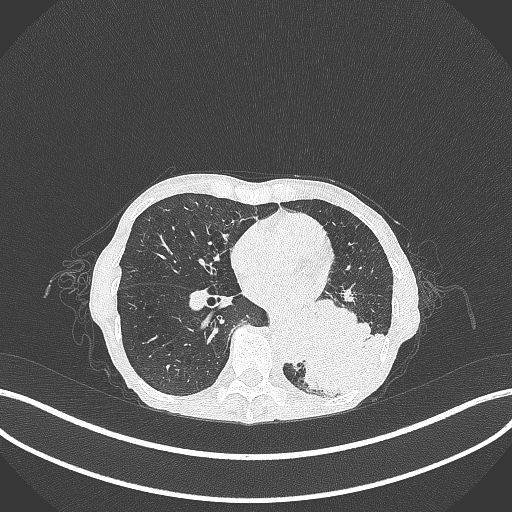
Chest CT, one axial slice; reconstruction kernel B70f; lung window (W 1500 / L -600 HU); 512 × 512 image matrix, field of view 400 × 400 mm. Female patient, age 70 years. From the clinical record (not read from this slice): clinical TNM (as recorded): T3 N0 M0; histopathological grade: G3.
Annotated regions visible in this slice (bounding box drawn by a radiologist):
- lung tumour (recorded histology: small cell carcinoma): bounding box [x1, y1, x2, y2] px = [296, 309, 389, 400]